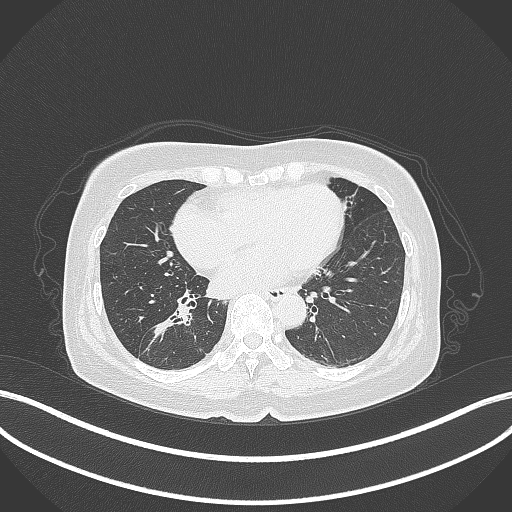
Chest CT, one axial slice; slice 161 of 429 in the series (ordered by position); reconstruction kernel B70f; 120 kVp; lung window (W 1500 / L -600 HU); 1 mm slice thickness; 512 × 512 image matrix, field of view 400 × 400 mm. Female patient, age 67 years. Case-level facts recorded for this patient, not image findings: clinical TNM (as recorded): T1c N1 M0.
Outlined on this slice (bounding box drawn by a radiologist):
- lung tumour (recorded histology: adenocarcinoma): bounding box <141,301,198,357> (left, top, right, bottom; pixels)